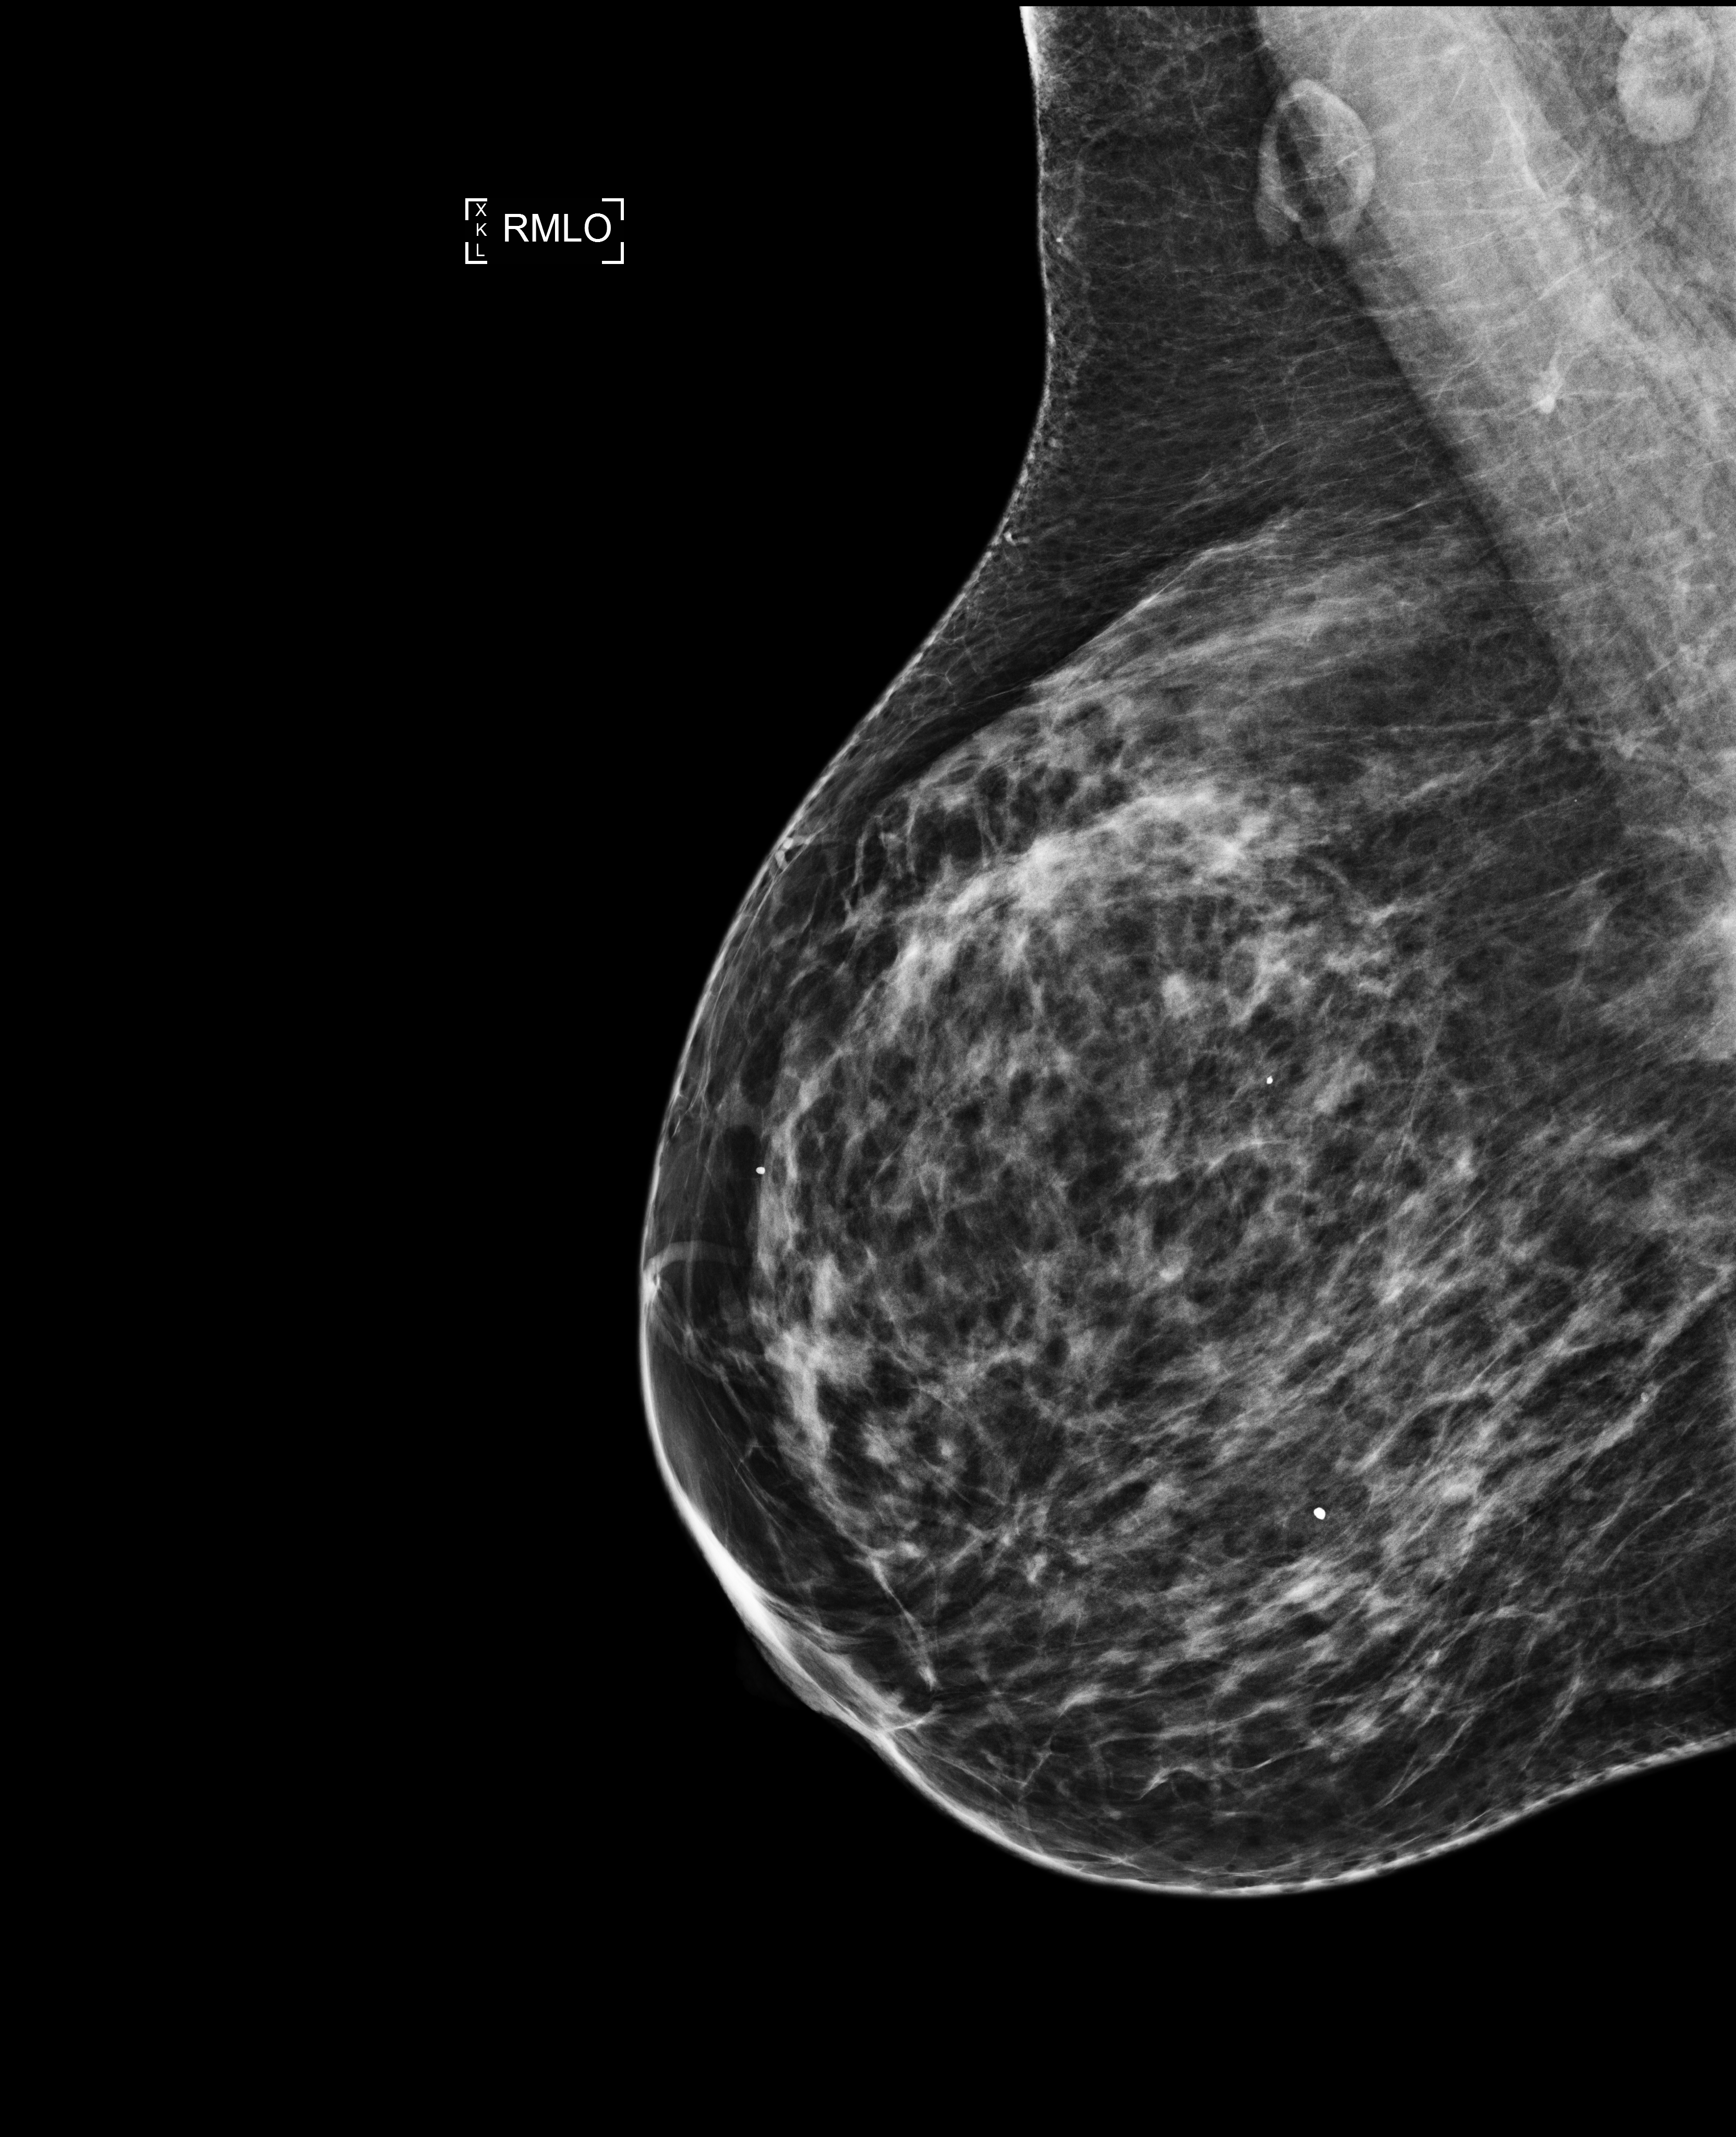
Screening examination. Patient aged 46 years (female).
Image type: full-field digital mammogram. Breast: right. Projection: mediolateral oblique (MLO) view.